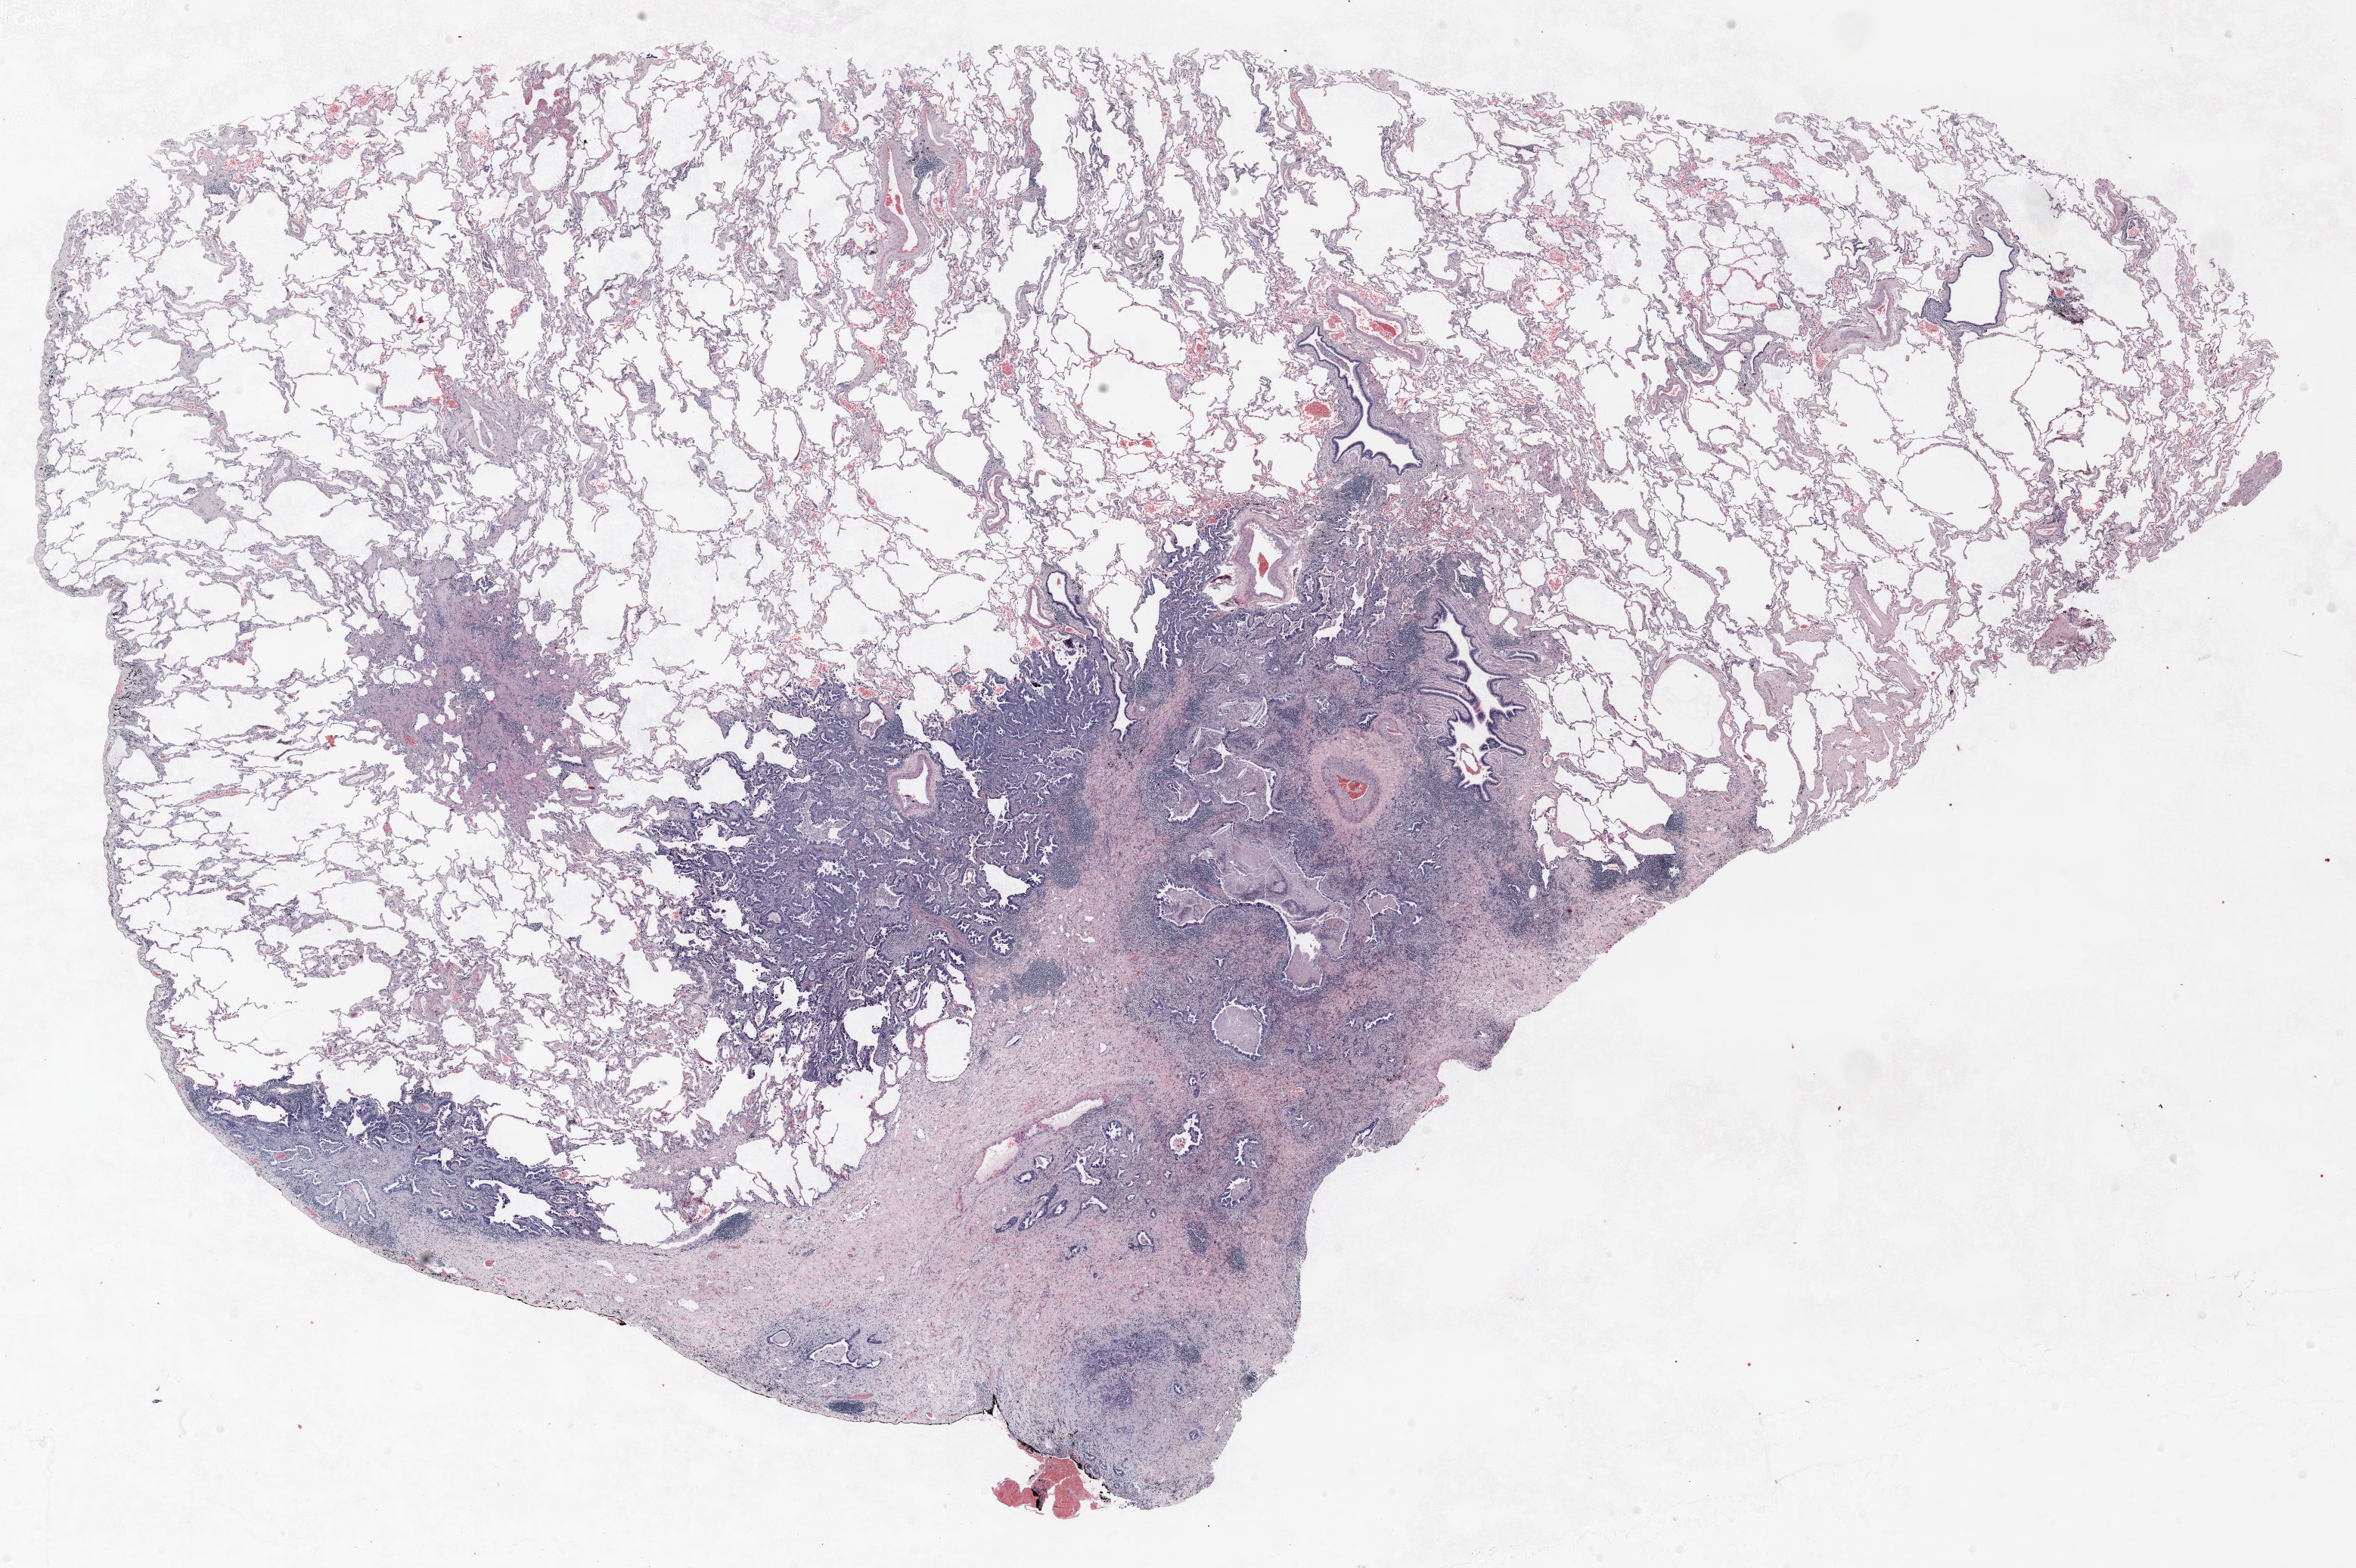
H&E whole-slide image, whole scanned area (about 25.0 x 16.7 mm, acquisition: 20x scan) shown as a low-resolution overview. FFPE section. Lung. Female patient, aged 68 at enrolment. Former smoker at enrolment. Grade: moderately differentiated (G2).
Primary tumour location (clinical record): right upper lobe. Tumour size (pathology): 31 mm. Stage (AJCC 6th edition): IB. Participant's lung-cancer diagnosis: Adenocarcinoma, NOS.